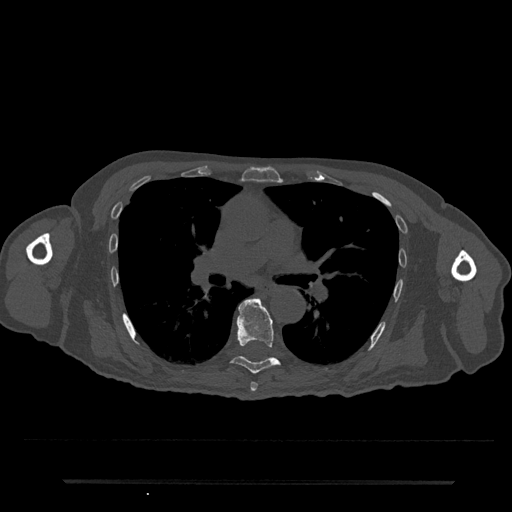
CT including the spine, one axial slice; position 481 of 797 along the scan axis; 120 kVp; bone window (W 1800 / L 400 HU); 0.5 mm slice thickness; 512 × 512 image matrix. Male patient, age 74 years. Case-level facts recorded for this patient, not image findings: primary cancer: prostate.
Annotated regions visible in this slice (semi-automatically segmented with operator editing):
- T6 vertebra: bounding box <250,382,258,392> (left, top, right, bottom; pixels)
- T7 vertebra: <231,298,280,374>